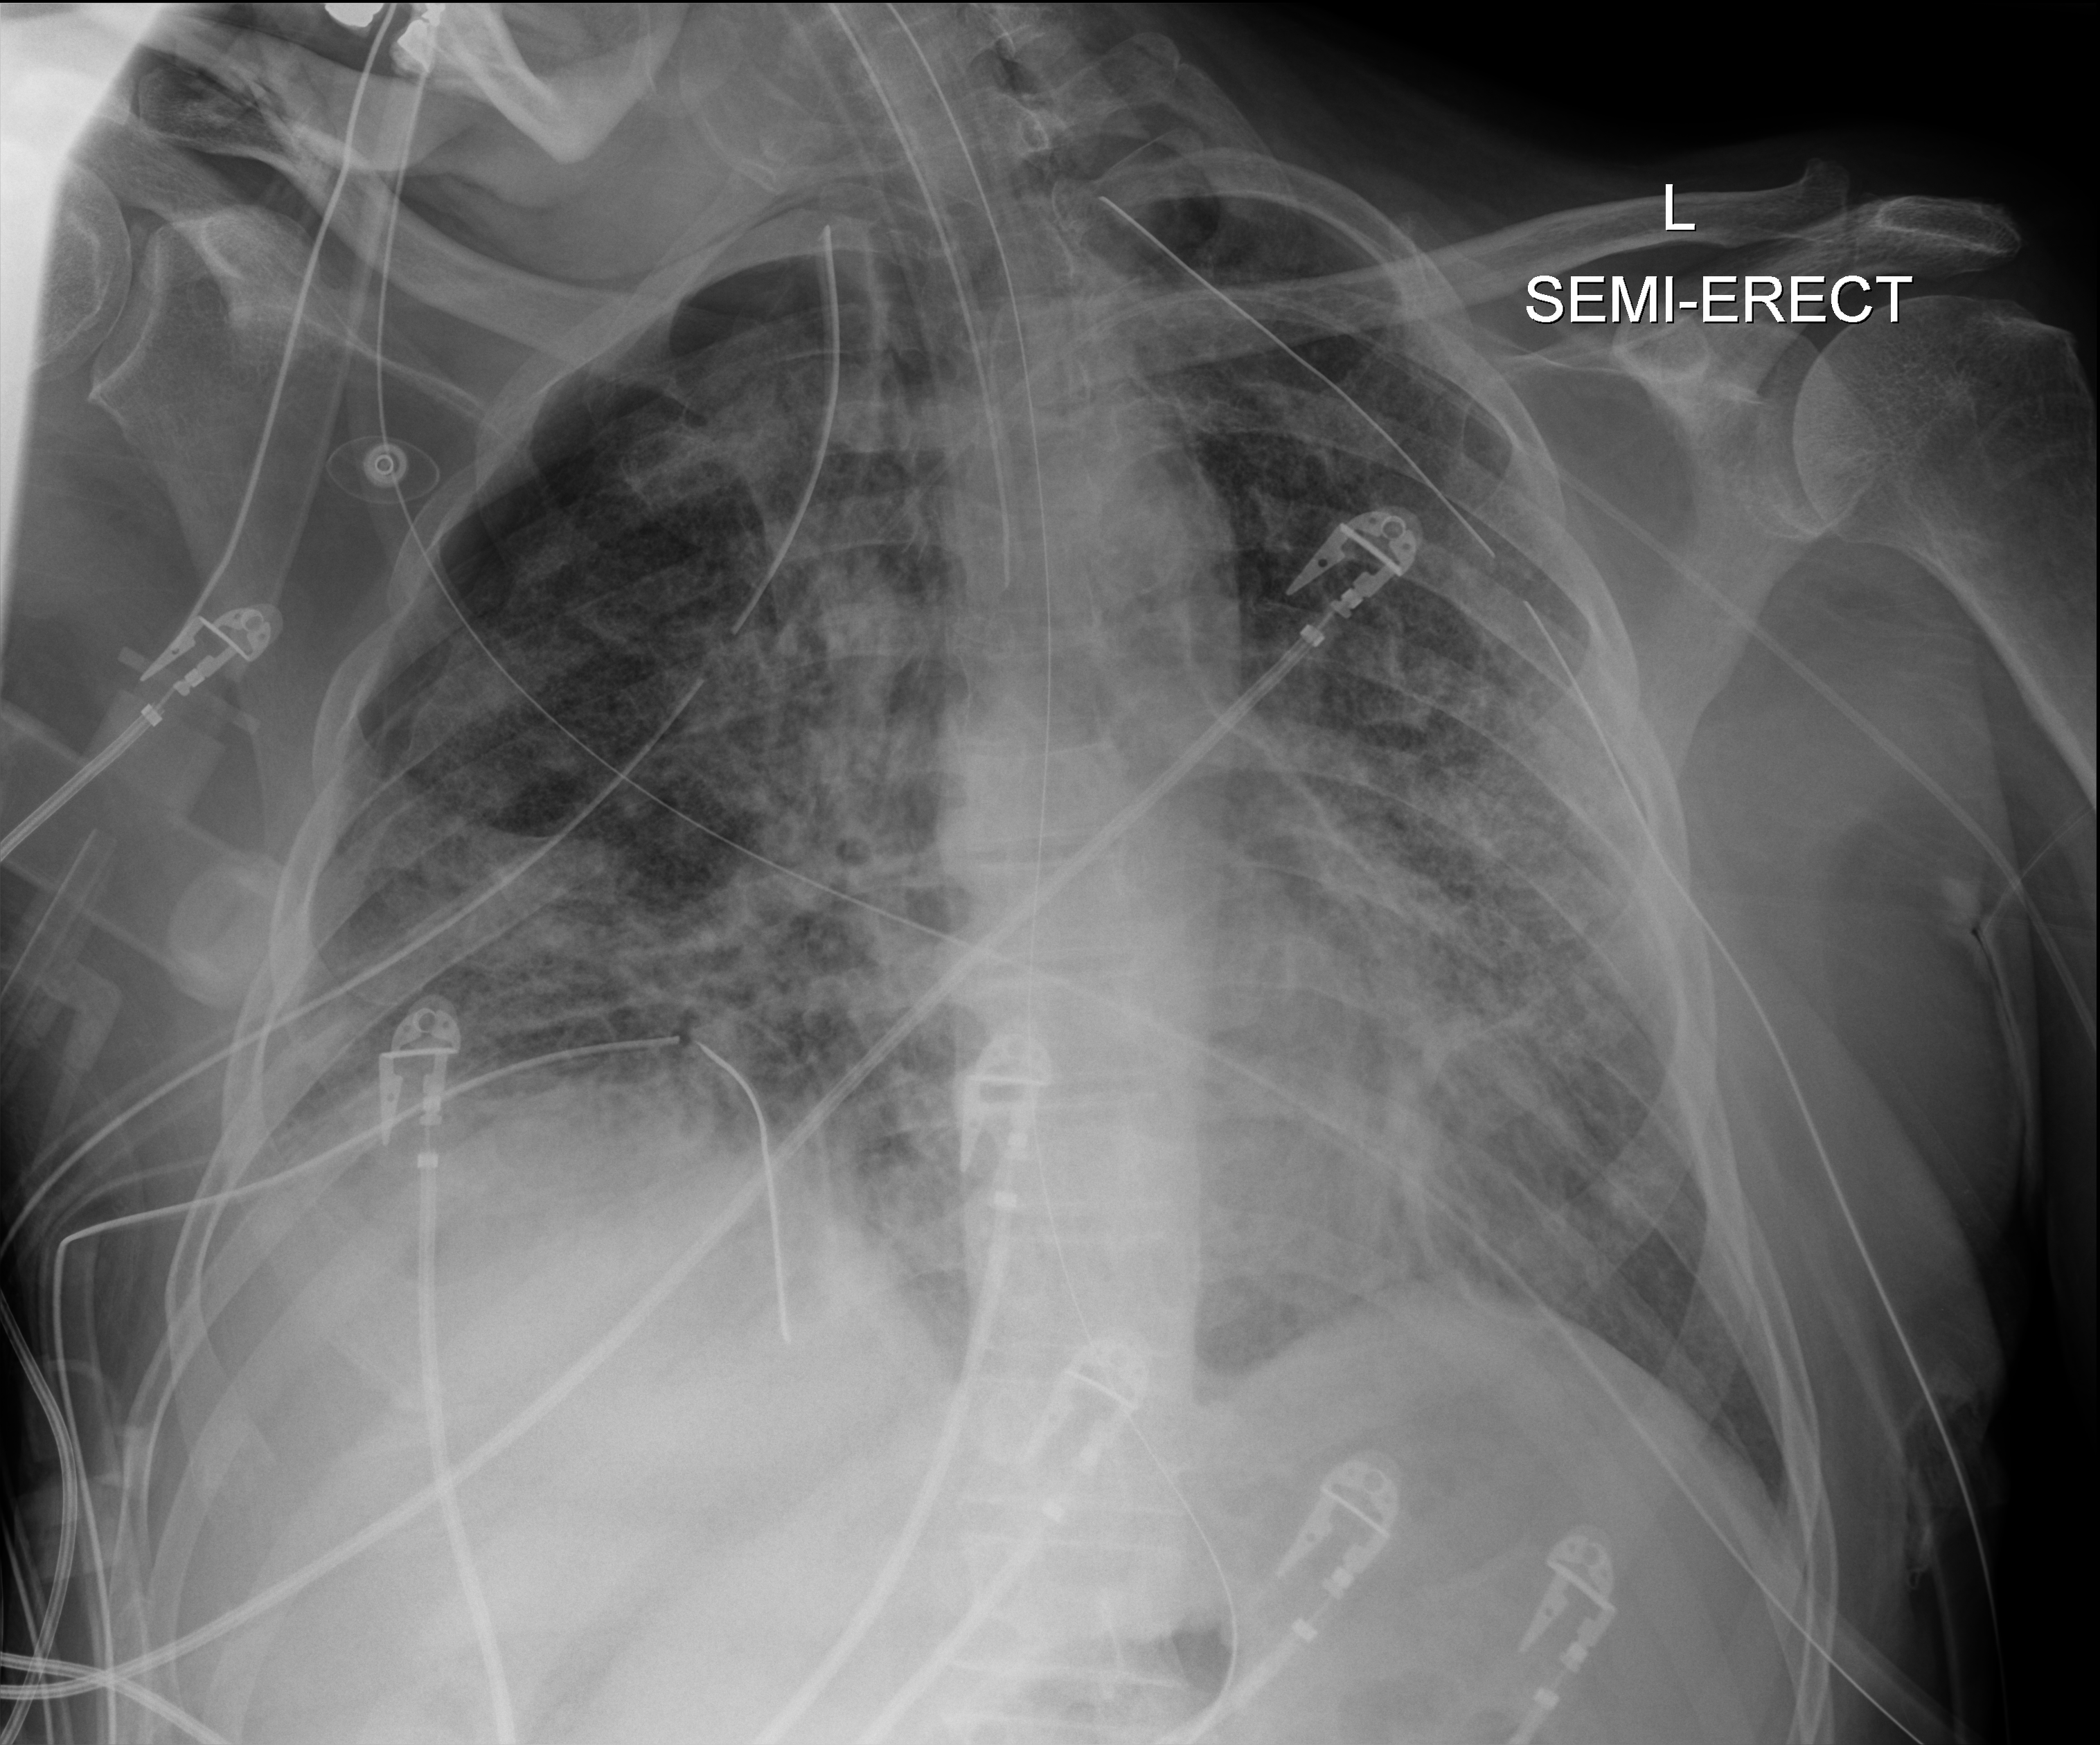
Bedside chest radiograph (digital radiography); anteroposterior (AP) projection. Male patient hospitalised with COVID-19, age 18–59 years.
Admission-level facts for this patient (not findings on this image; timing relative to this image not recorded):
- mechanically ventilated during this hospital stay: yes